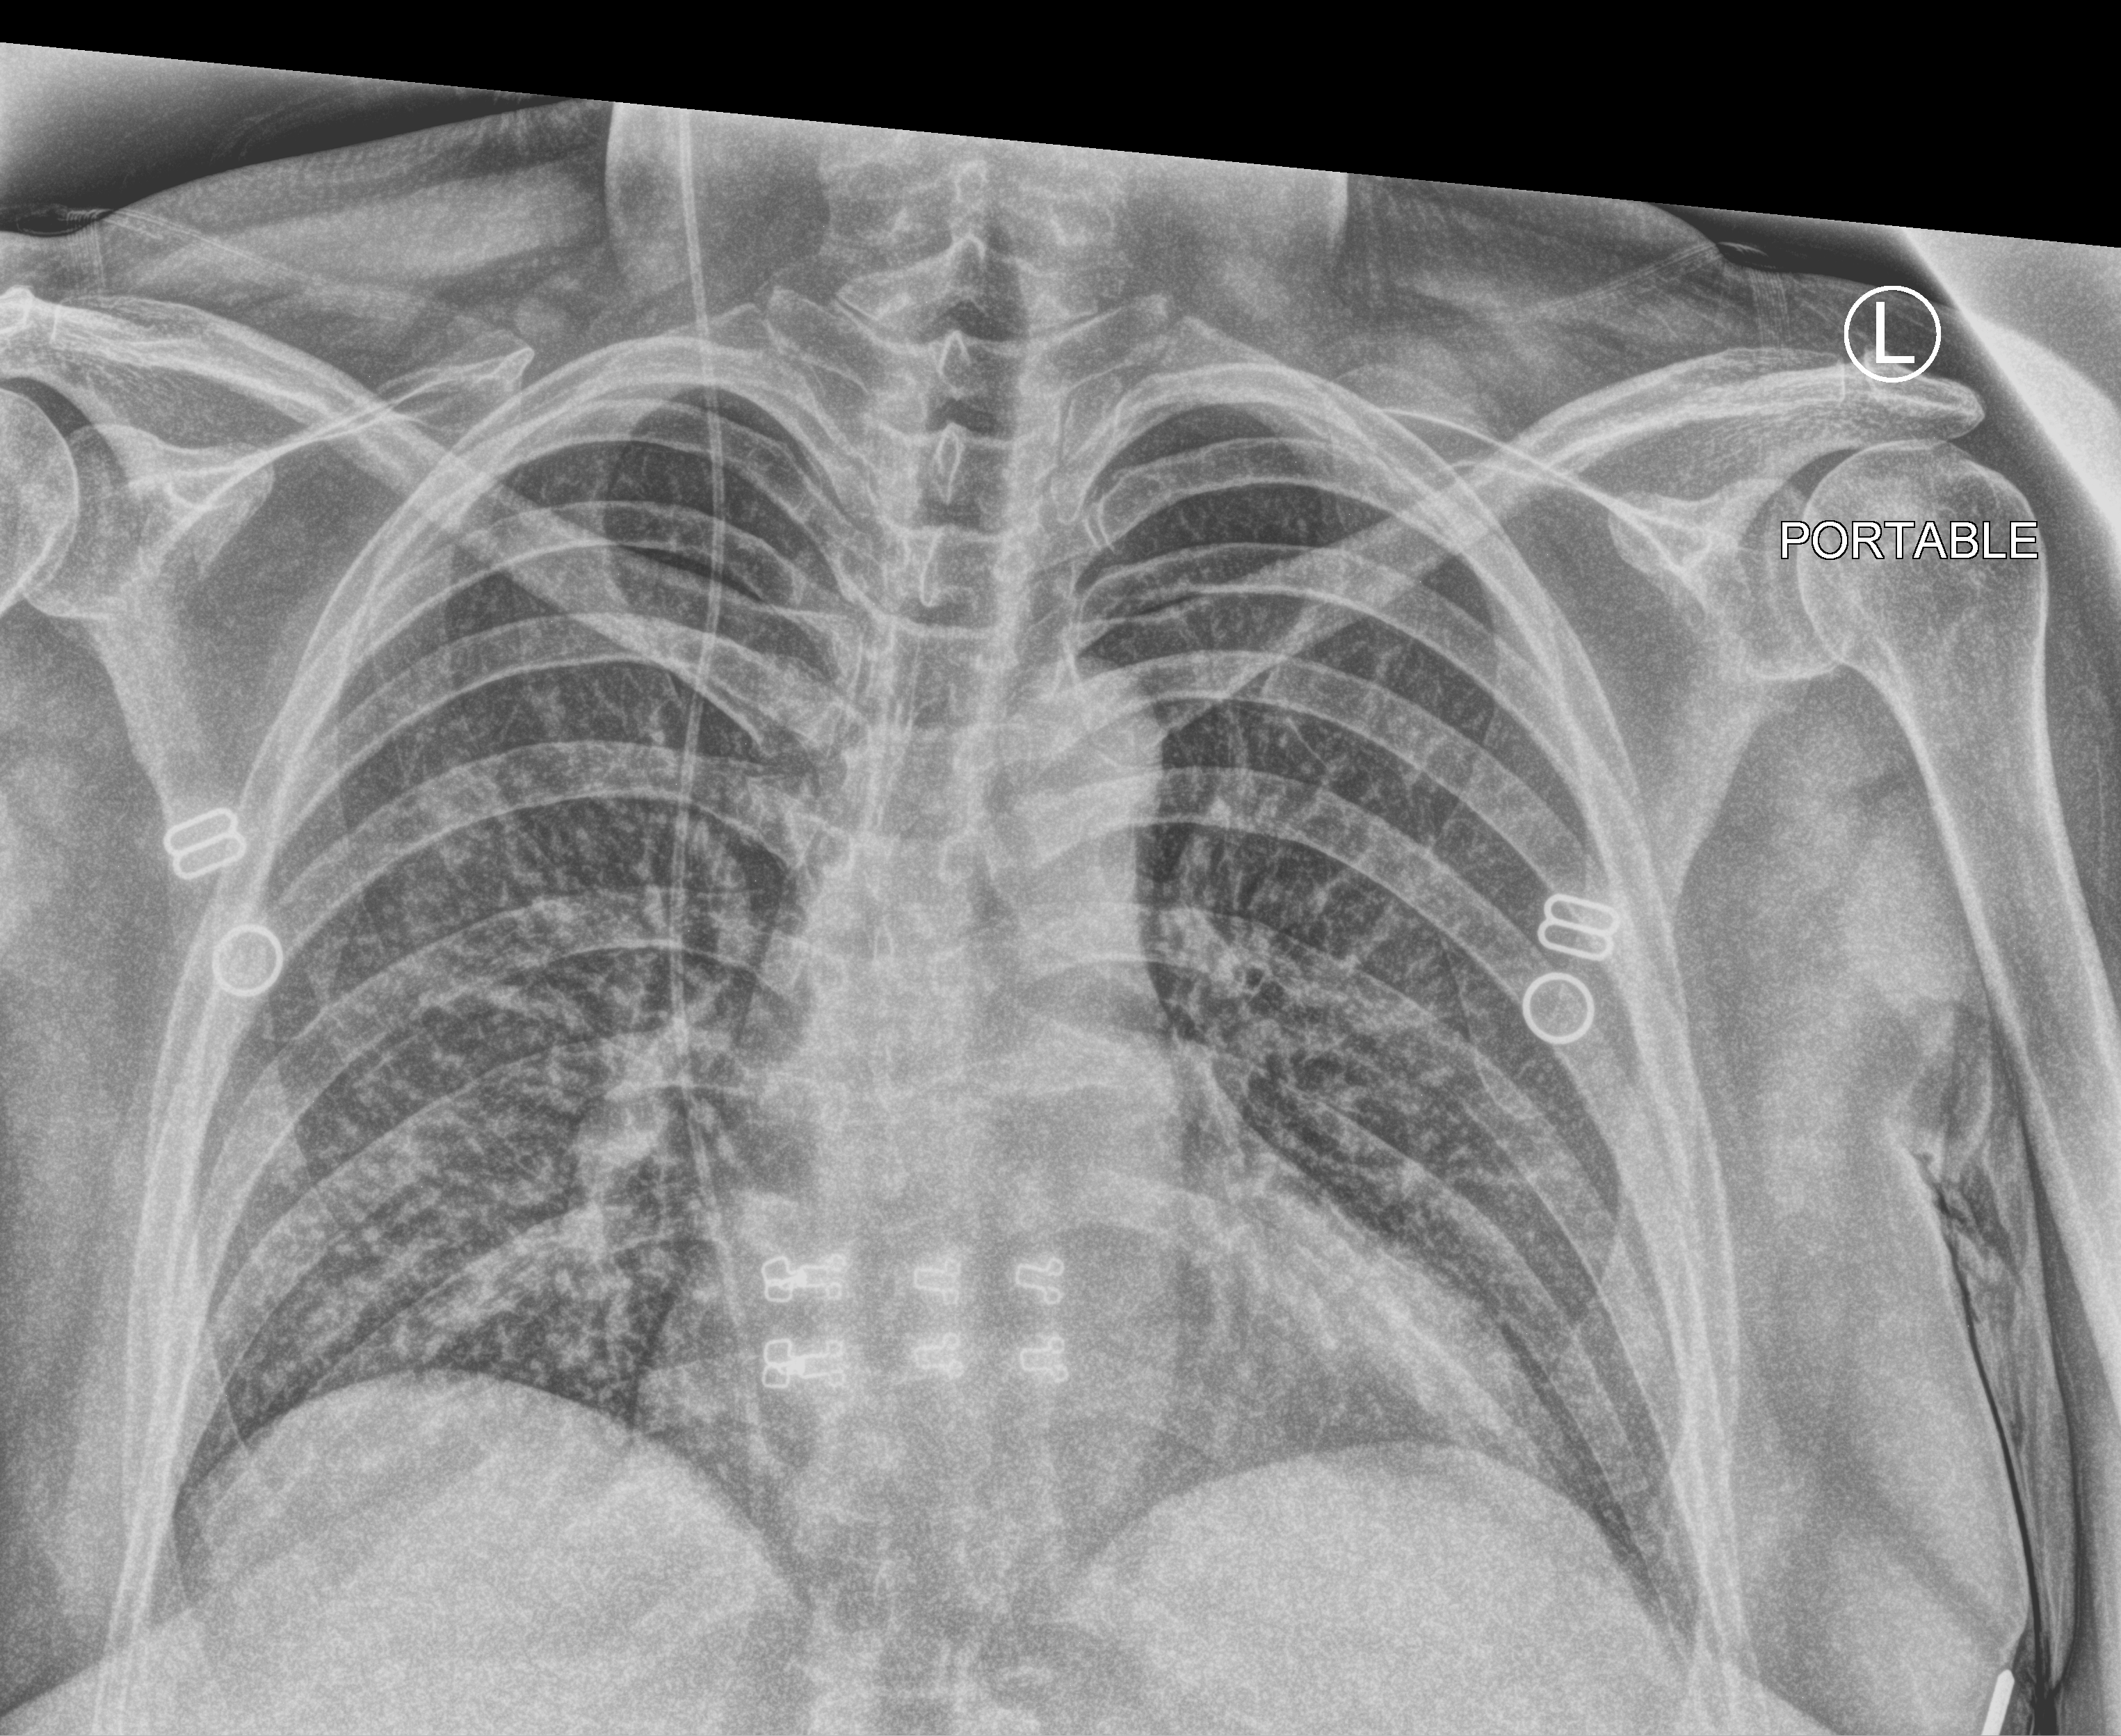
Chest X-ray (portable), anteroposterior (AP) projection. Patient hospitalised with COVID-19; female, aged 18–59 years.
From the hospital-stay record, not from the radiograph (when in the stay this image was taken is not recorded): mechanically ventilated during this hospital stay: no.